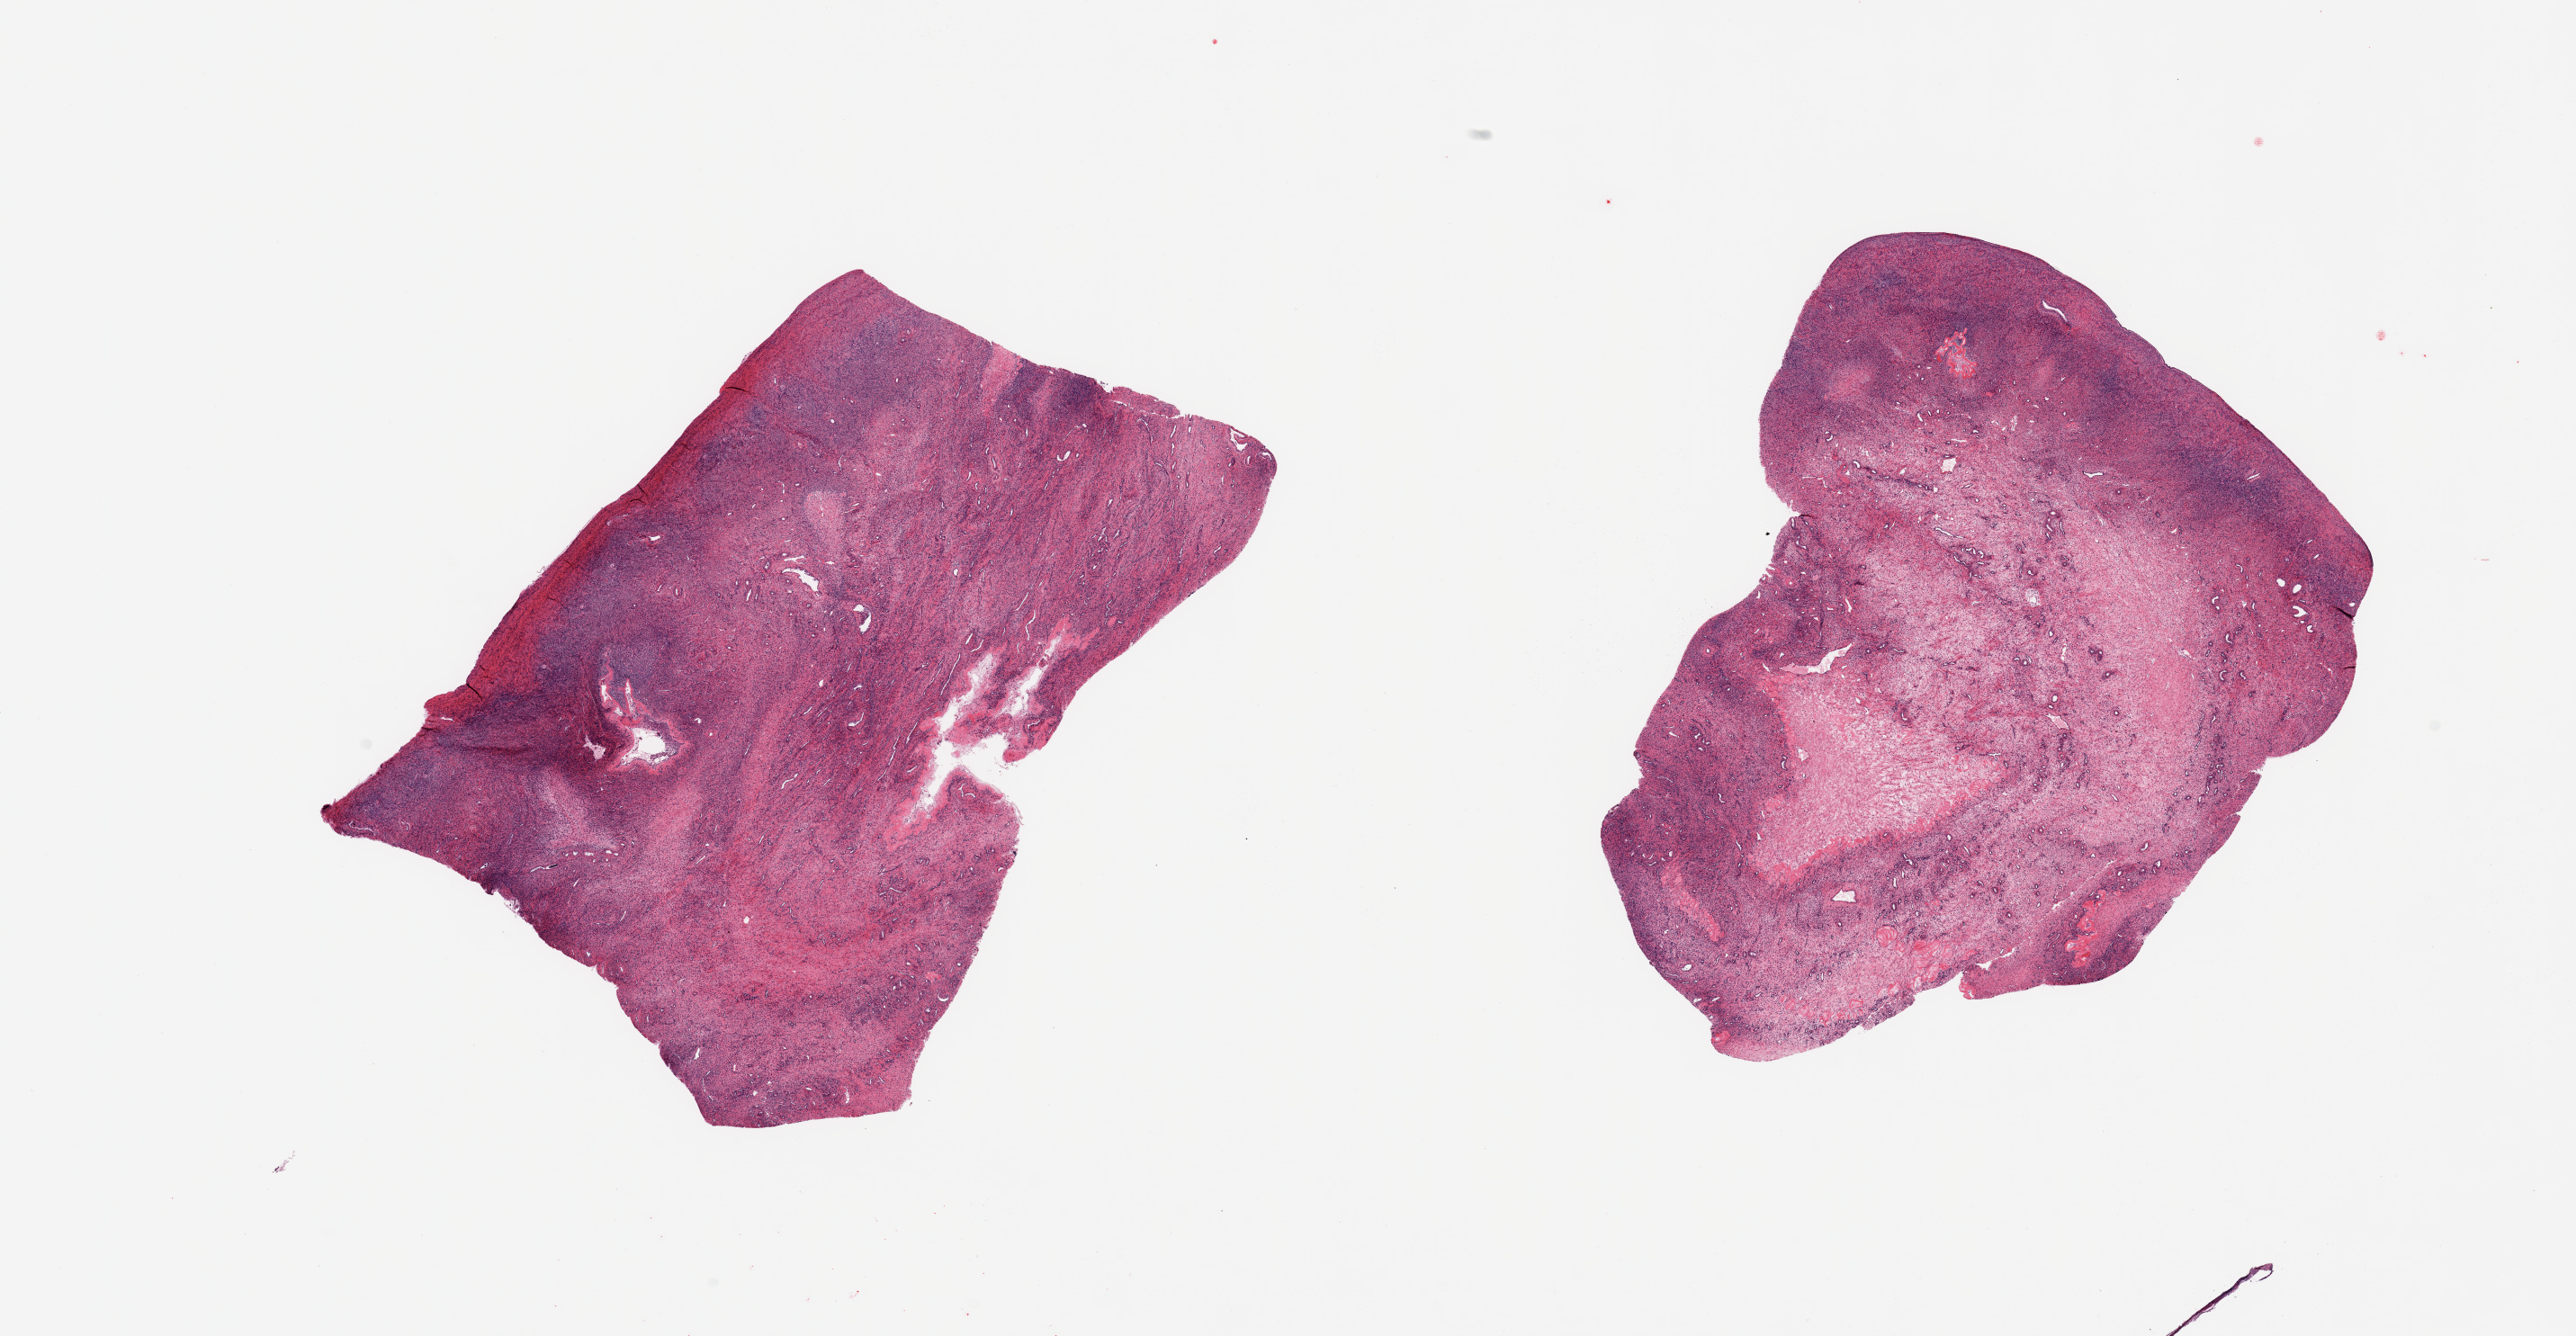
Whole-slide image, haematoxylin and eosin stain — a low-resolution overview of the entire scanned area, about 22.6 x 11.7 mm; PAXgene-fixed, paraffin-embedded tissue; section of ovary (target tissue); donor tissue sample. Donor sex: female.
Reviewer comment on this tissue sample: 2 pieces; plentiful ova in outer portion.